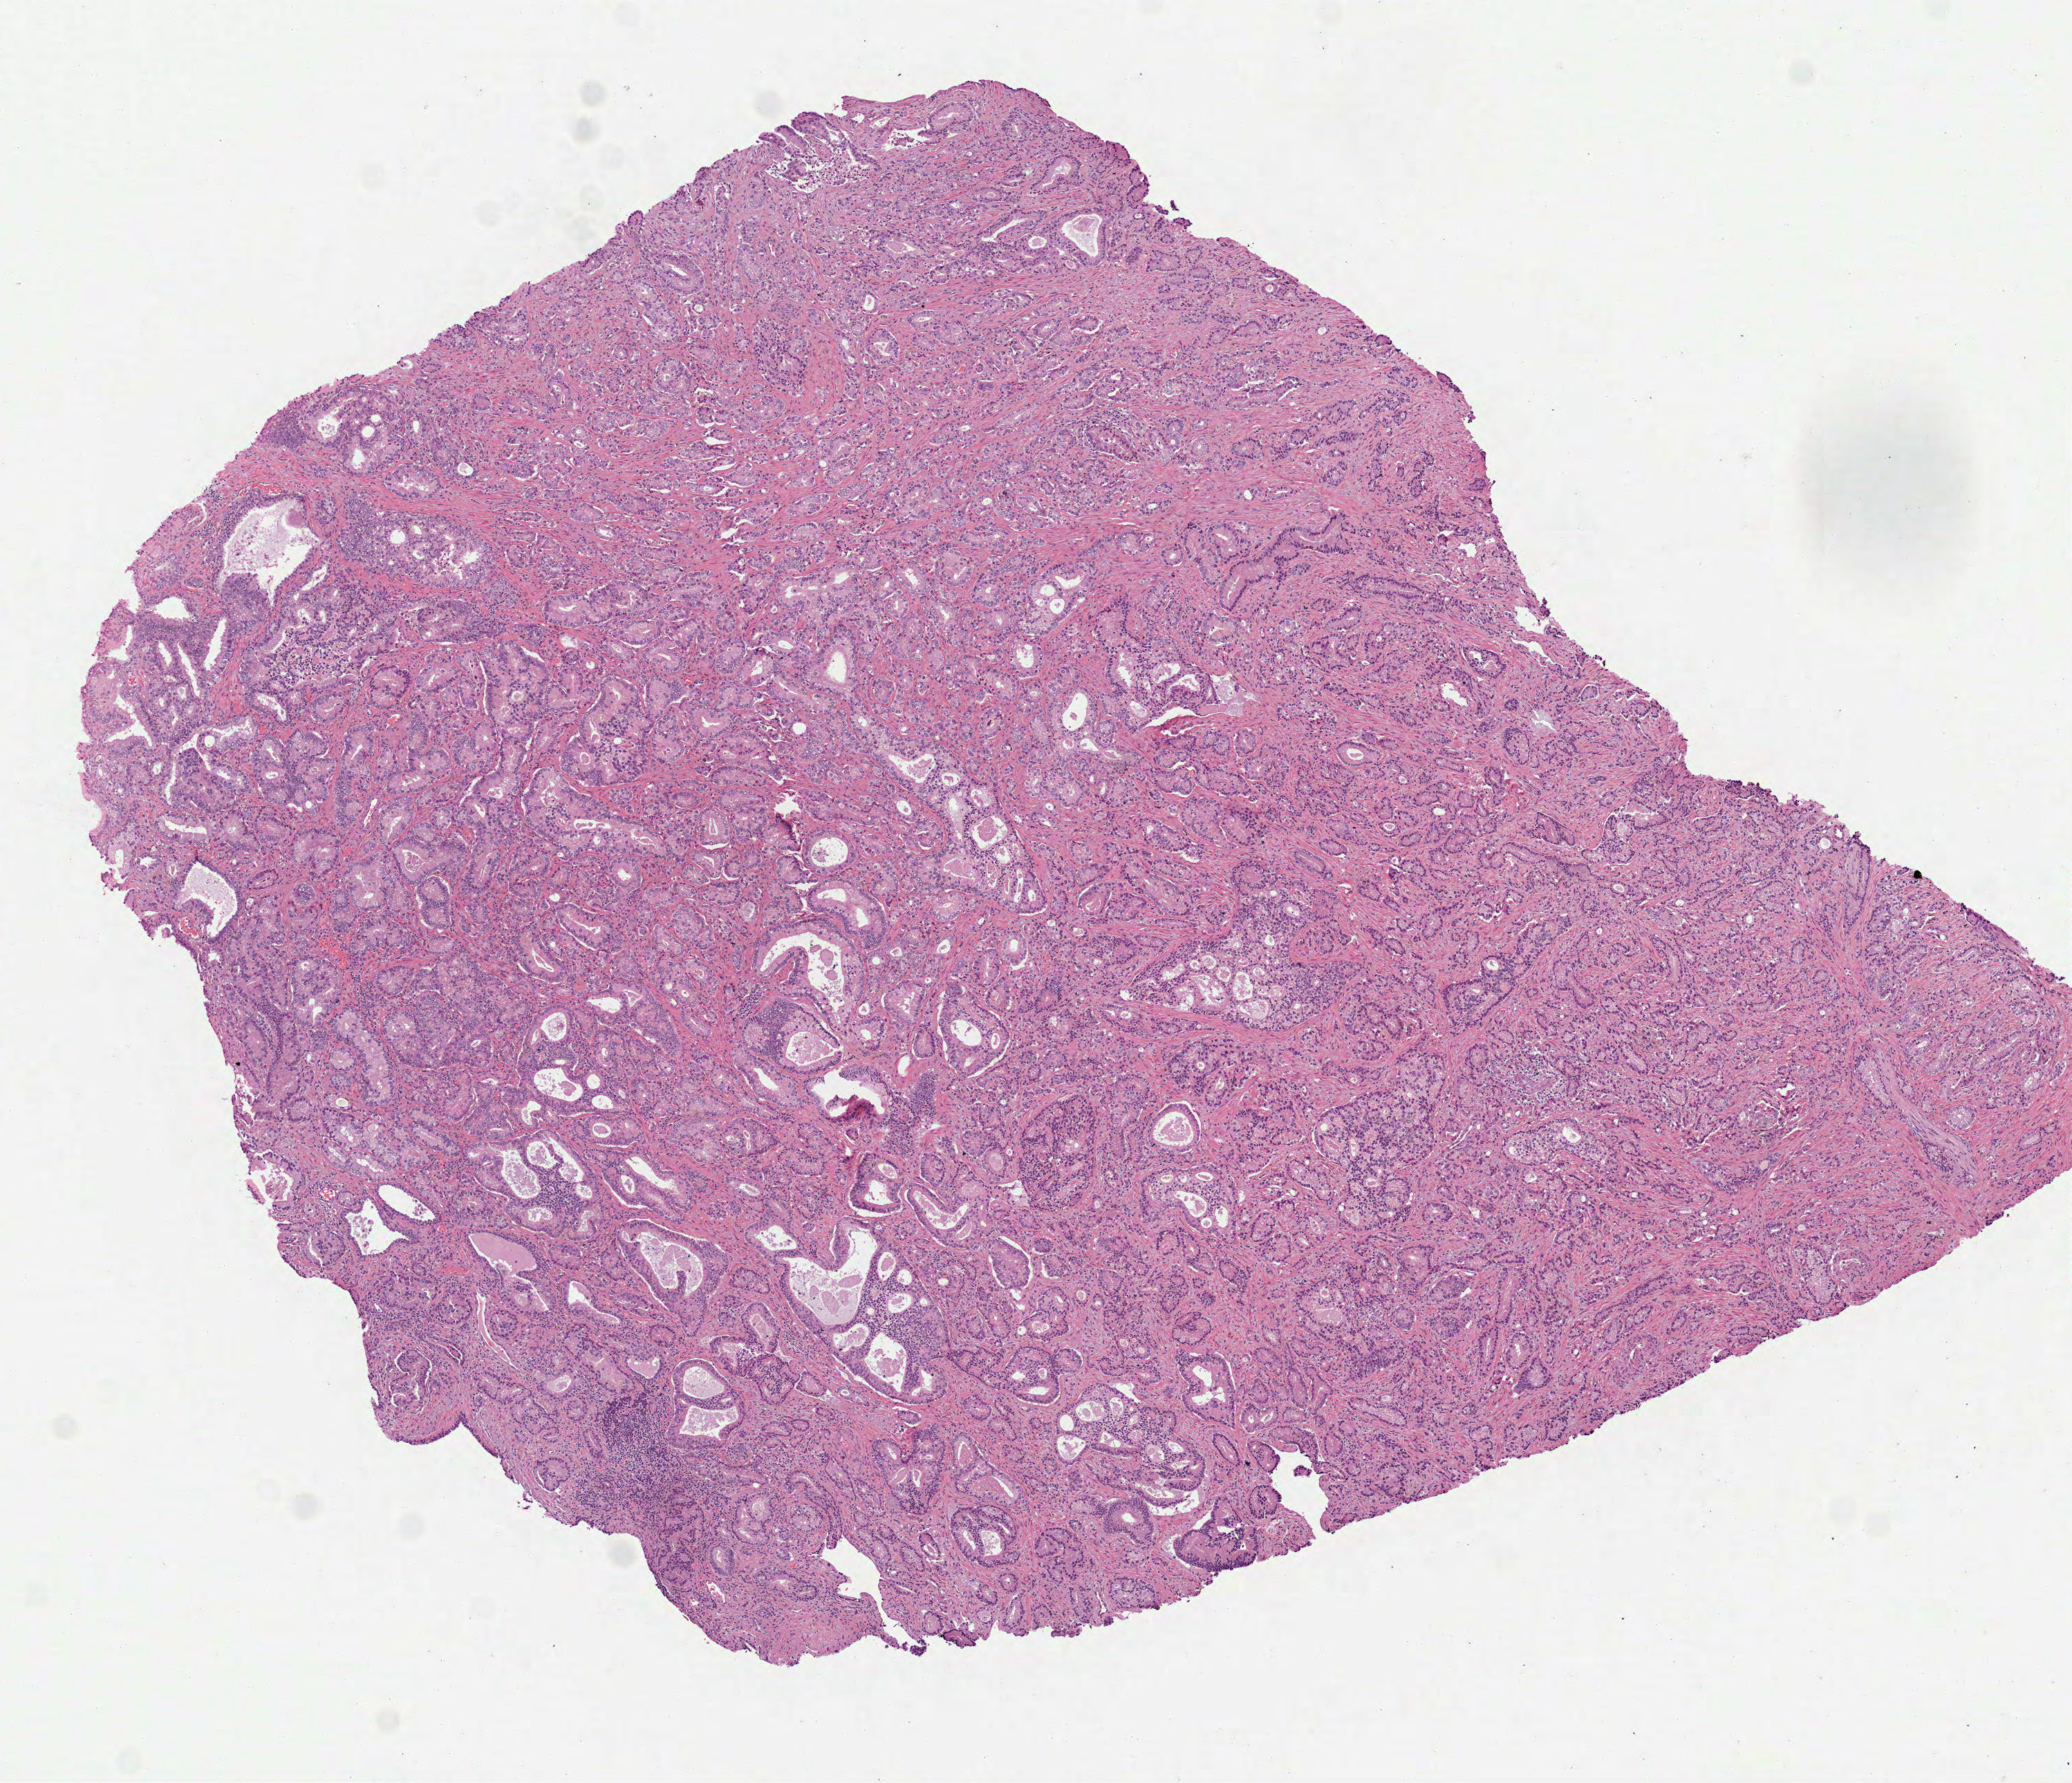
H&E whole-slide image, a low-resolution overview of the entire scanned area, about 6.0 x 5.2 mm. Formalin-fixed paraffin-embedded (FFPE) diagnostic section. Sample: primary tumour, prostate. Male, age 66 years at initial diagnosis. Gleason score: 8 (3+5).
Pathologic diagnosis: Acinar cell carcinoma (prostate gland).